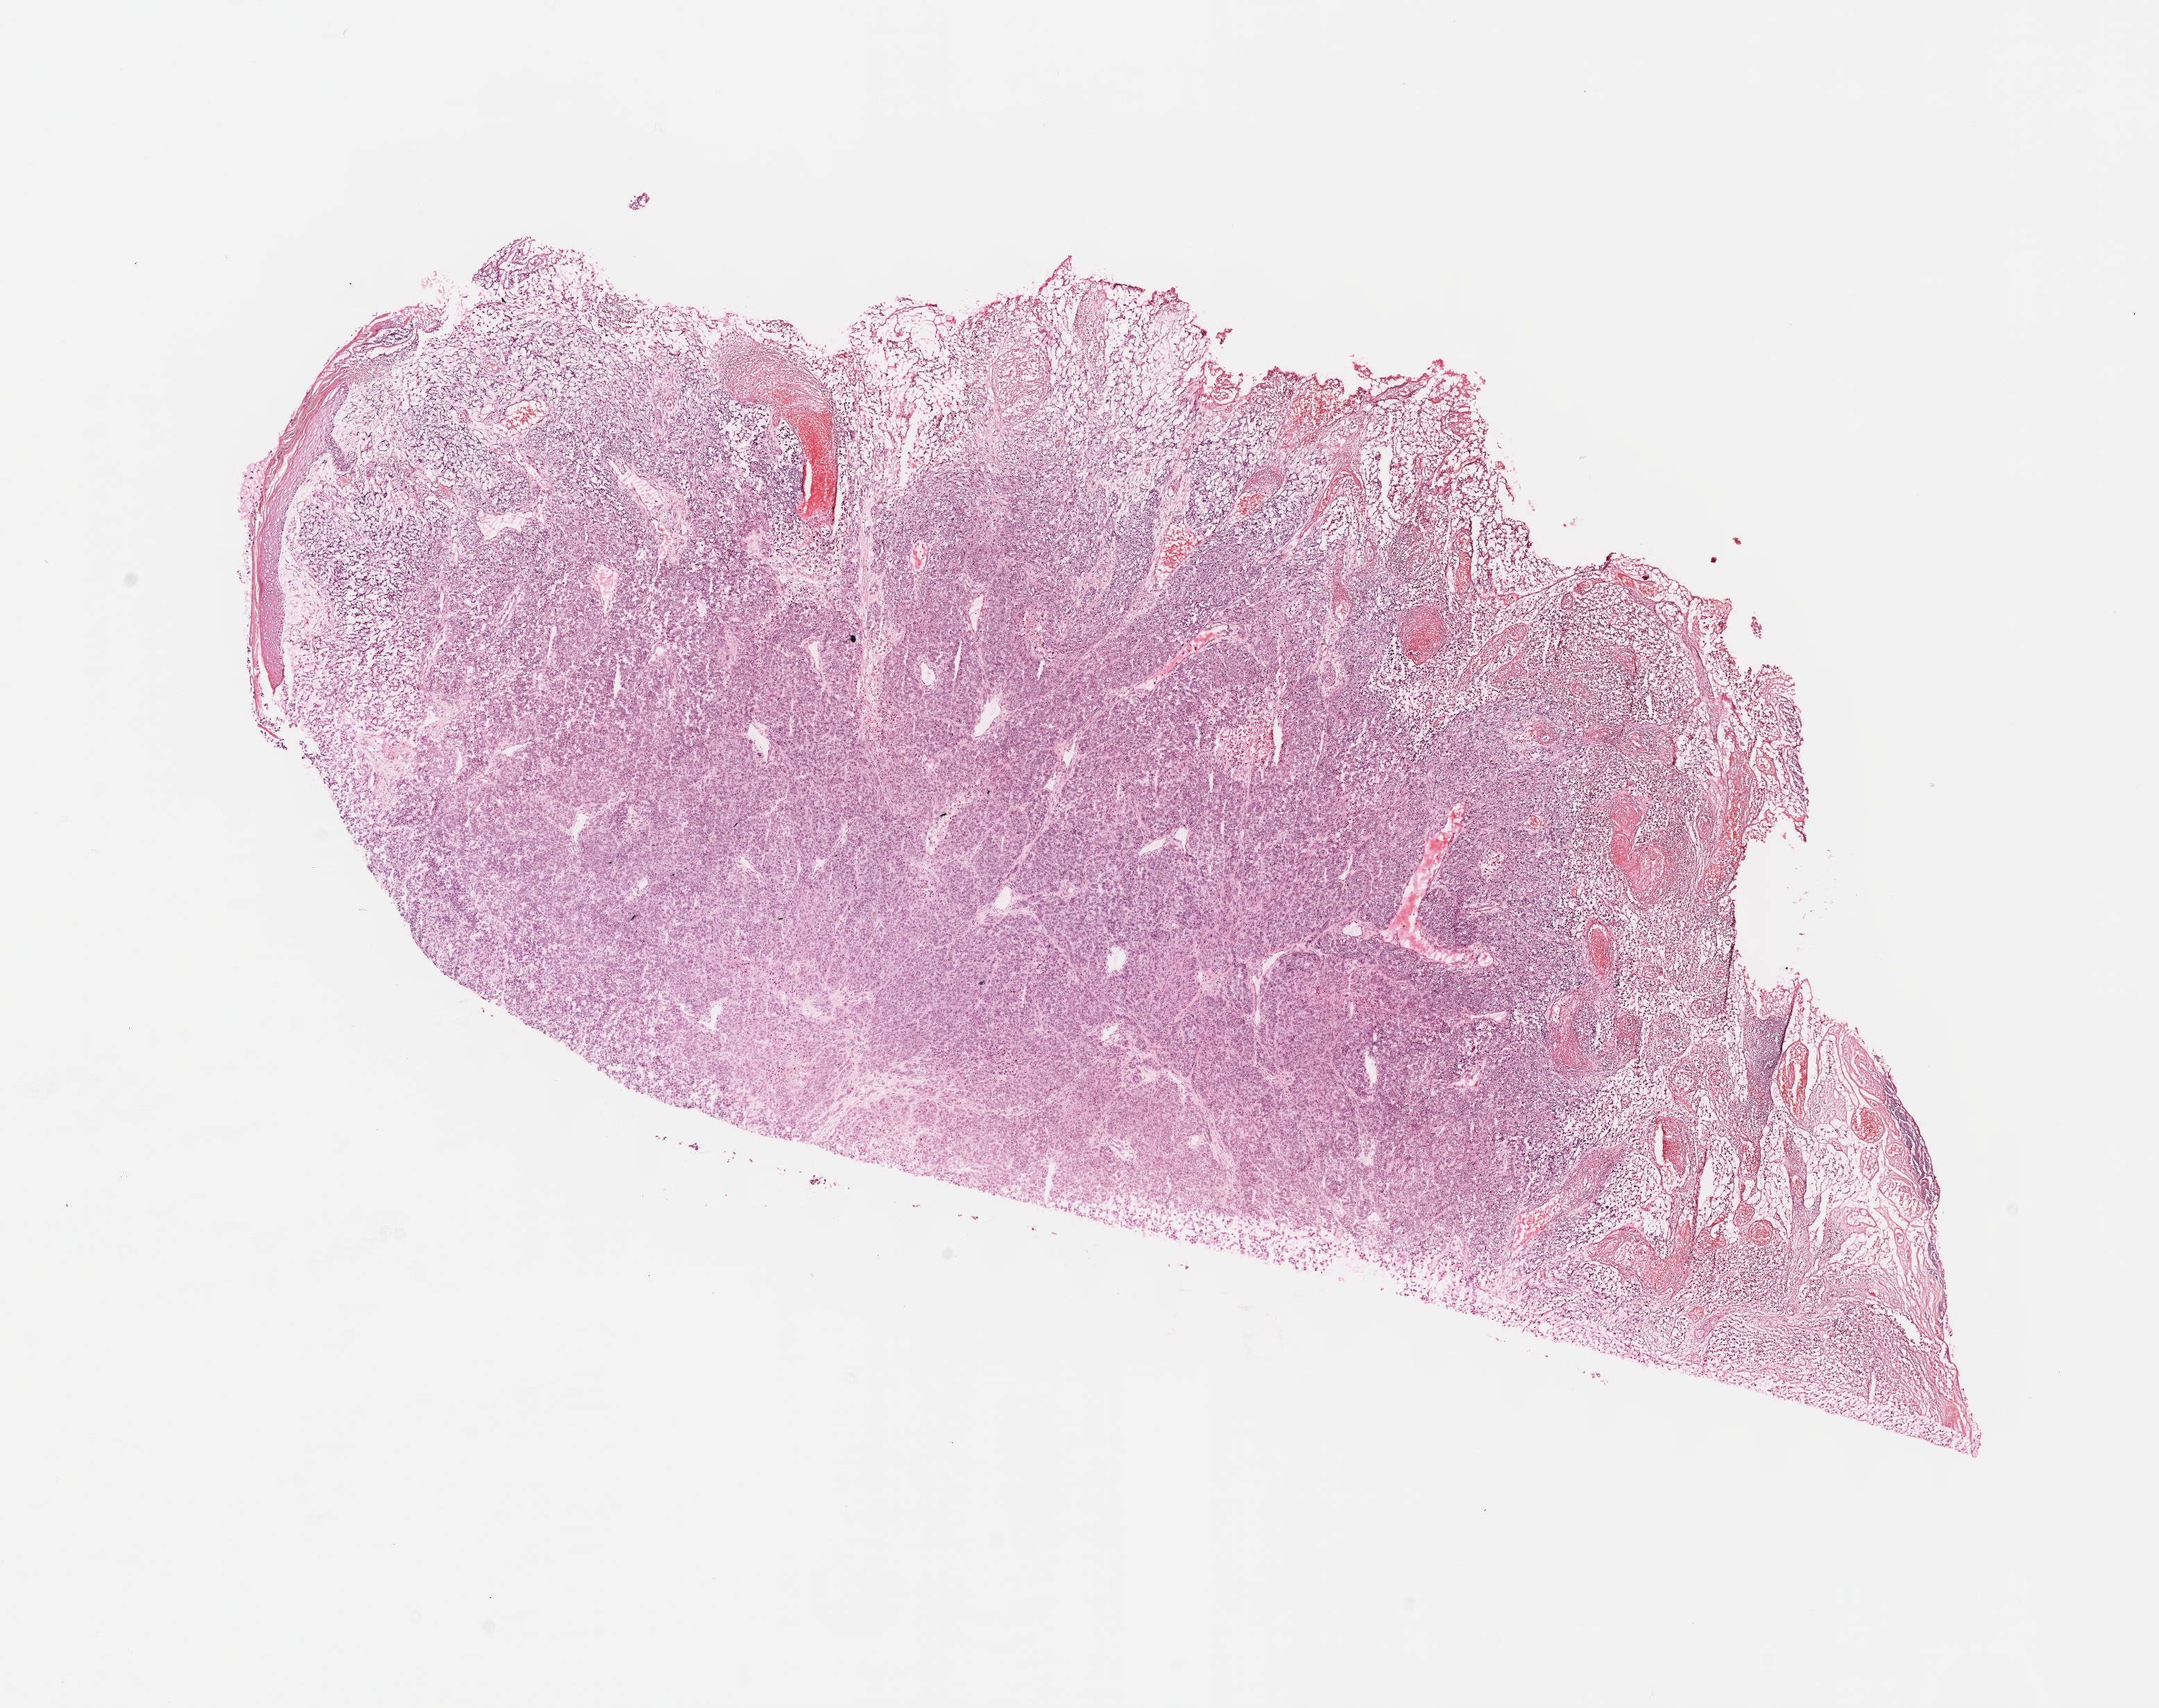
Hematoxylin and eosin (H&E) stained whole-slide image, low-resolution overview of the scanned area, about 12.6 x 9.9 mm. FFPE section. Skin, primary tumour sample. Male, age 63 years at initial diagnosis.
* AJCC pathologic stage: IIA (7th edition)
* diagnosis: Malignant melanoma, NOS